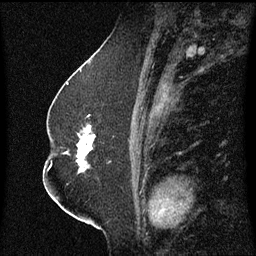
Breast MRI (dynamic contrast-enhanced), one sagittal slice. Position 32 of 60 along the scan axis. Dynamic contrast-enhanced series, image 2 of 3 at this slice position (ordered by acquisition). 1.5 T. TE 4.2 ms, TR 8.4 ms. 2.3 mm slice thickness. 256 × 256 image matrix, field of view 200 × 200 mm. Patient: female, 52 years. From the clinical record (not read from this slice): setting: breast cancer imaged before/during neoadjuvant chemotherapy; receptor status: HR-positive, HER2-negative.
Structures marked on this image (semi-automatic segmentation, software-assisted and operator-edited):
- analysis volume of interest (the breast-tissue region the enhancement analysis was run in; not a lesion): bounding box [x1, y1, x2, y2] px = [66, 124, 116, 175]
- tumour enhancement mask (voxels above the 70 % enhancement threshold inside the analysis volume of interest): [77, 126, 96, 173]